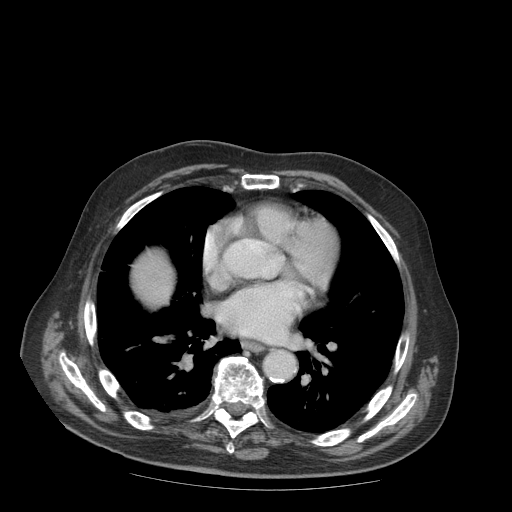
Contrast-enhanced abdominal CT (liver protocol), one axial slice. Slice 97 of 99 in the series (ordered by position). Reconstruction kernel STANDARD. 140 kVp. Soft-tissue window (W 400 / L 40 HU). 2.5 mm slice thickness. 512 × 512 image matrix, field of view 420 × 420 mm. Case-level facts recorded for this patient, not image findings: diagnosis: hepatocellular carcinoma (patient treated with transarterial chemoembolisation; whether this scan precedes or follows treatment is not stated here); TNM stage (as recorded): Stage-IIIB; Child-Pugh class: A; tumour differentiation: well differentiated.
Annotated regions visible in this slice (semi-automatic segmentation, software-assisted and operator-edited):
- liver parenchyma outside the tumour (the mass and vessels are separate outlines, so this box may not span the whole liver): bounding box [x1, y1, x2, y2] px = [132, 250, 172, 306]